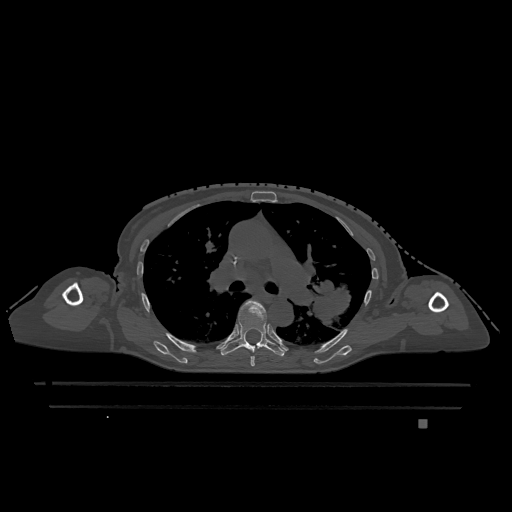
CT including the spine, one axial slice; position 803 of 1317 along the scan axis; bone window (W 1800 / L 400 HU); 512 × 512 image matrix, field of view 500 × 500 mm. Female patient, age 74 years. Case-level facts recorded for this patient, not image findings: primary cancer: lung.
Outlined on this slice (semi-automatic segmentation, software-assisted and operator-edited):
- T5 vertebra: bounding box (x1, y1, x2, y2) in pixels: (250, 356, 255, 367)
- T6 vertebra: (220, 300, 285, 357)